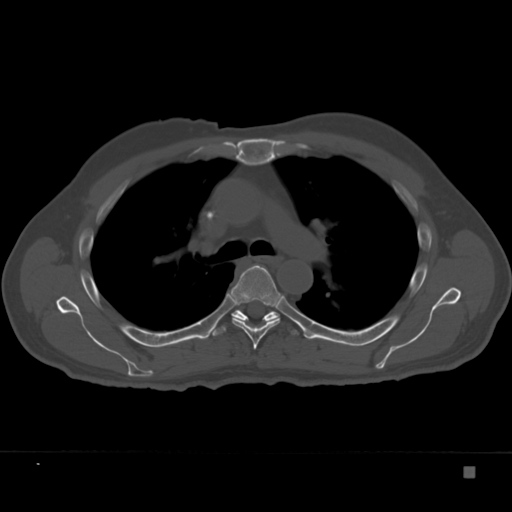
CT including the spine, one axial slice; position 251 of 332 along the scan axis; bone window (W 1800 / L 400 HU); 1.5 mm slice thickness; 512 × 512 image matrix. Patient: male, 72 years. Case-level facts recorded for this patient, not image findings: primary cancer: skeletal.
Annotated regions visible in this slice (semi-automatically segmented with operator editing):
- T5 vertebra: box from (x=227, y=265) to (x=285, y=350) px
- T6 vertebra: (x=212, y=309)–(x=299, y=337)